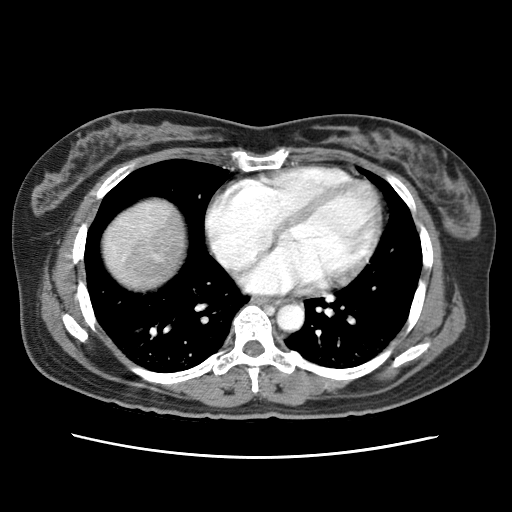
Contrast-enhanced abdominal CT (liver protocol), one axial slice; slice 71 of 79 in the series (ordered by position); 120 kVp; soft-tissue window (W 400 / L 40 HU); 512 × 512 image matrix, field of view 340 × 340 mm. From the clinical record (not read from this slice): diagnosis: hepatocellular carcinoma (patient treated with transarterial chemoembolisation; whether this scan precedes or follows treatment is not stated here); TNM stage (as recorded): Stage-I; Child-Pugh class: A; tumour differentiation: moderately differentiated; tumour nodularity: uninodular.
Outlined on this slice (semi-automatic segmentation, software-assisted and operator-edited):
- abdominal aorta: bounding box <277,303,303,331> (left, top, right, bottom; pixels)
- liver parenchyma outside the tumour (the mass and vessels are separate outlines, so this box may not span the whole liver): <104,198,183,288>